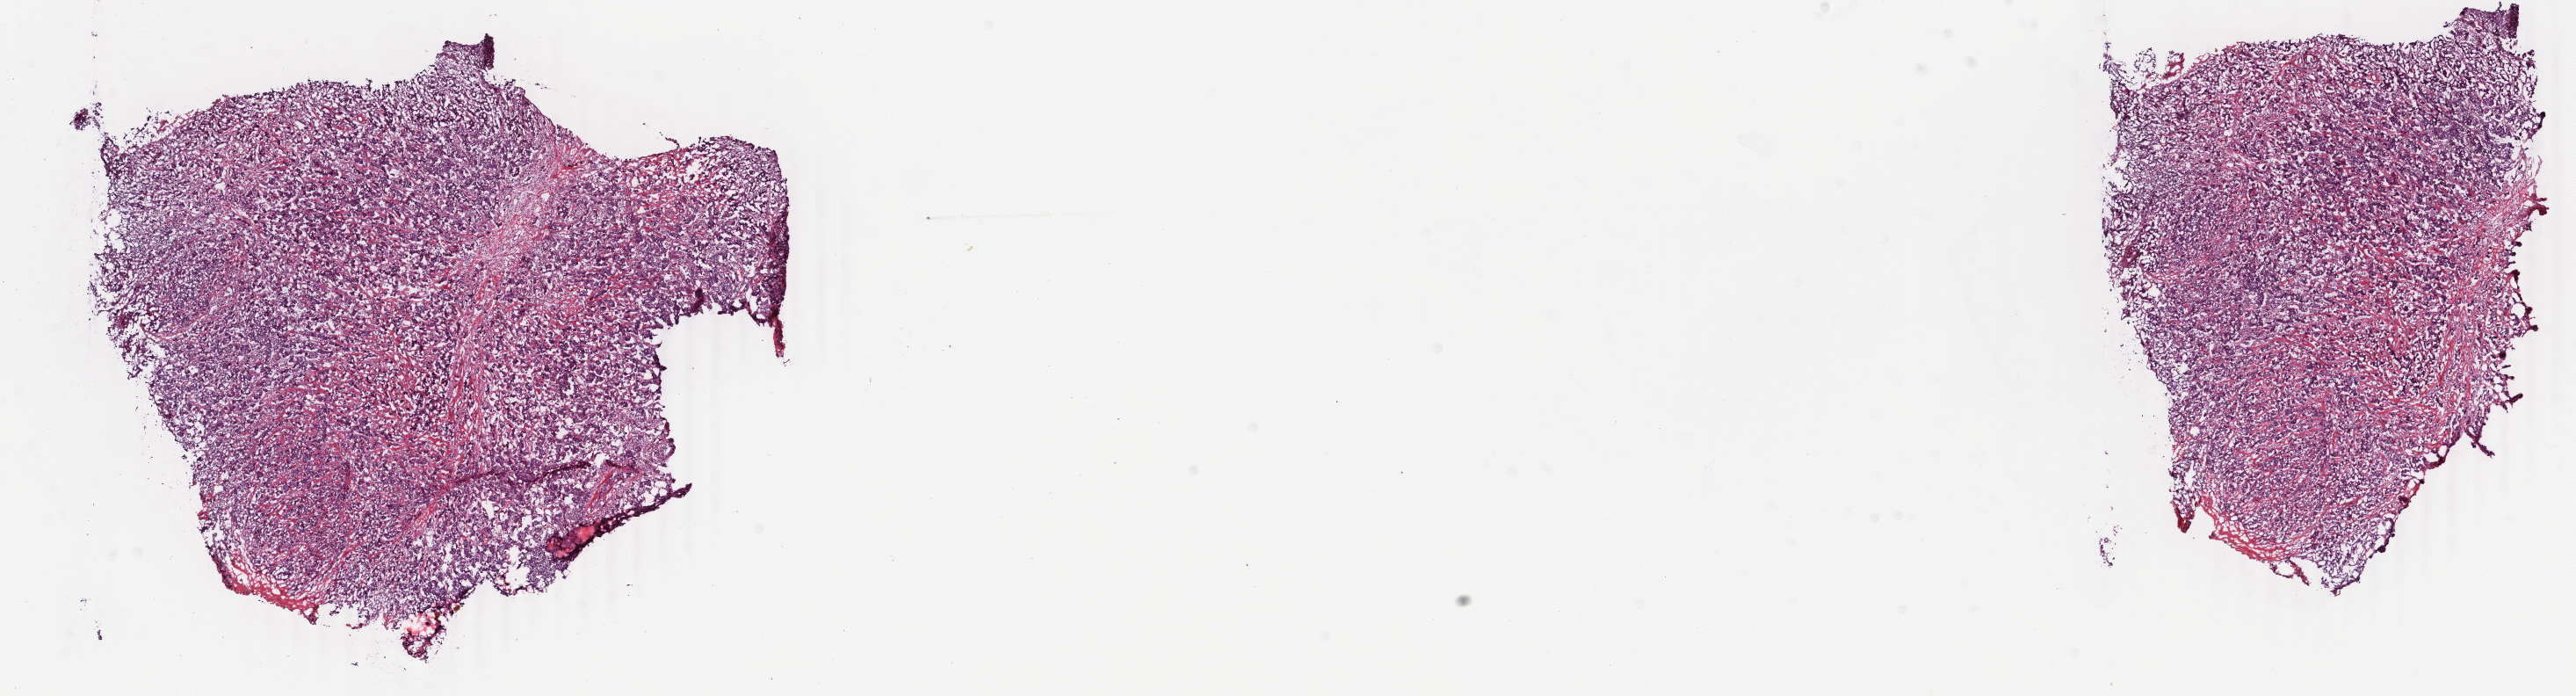
H&E whole-slide image, a low-resolution overview of the entire scanned area, about 23.3 x 6.3 mm. Frozen section. Sample: primary tumour, breast. Patient: female, age at initial diagnosis 68 years.
Histologic diagnosis: Infiltrating duct carcinoma, NOS.